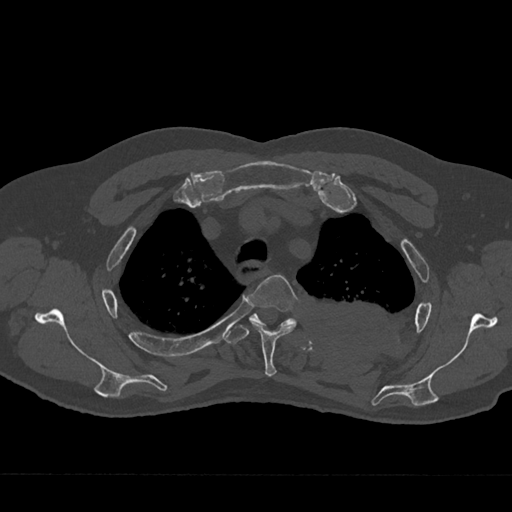
CT including the spine, one axial slice; slice 550 of 797 in the series (ordered by position); reconstruction kernel Br40s/3; 120 kVp; bone window (W 1800 / L 400 HU); 0.5 mm slice thickness; 512 × 512 image matrix. Patient: male, 75 years. From the clinical record (not read from this slice): primary cancer: renal; vertebrae with lytic lesions (as recorded): T4.
Structures marked on this image (semi-automatic segmentation, software-assisted and operator-edited):
- T3 vertebra: bounding box [x1, y1, x2, y2] px = [248, 275, 300, 377]
- T4 vertebra: [225, 314, 297, 344]